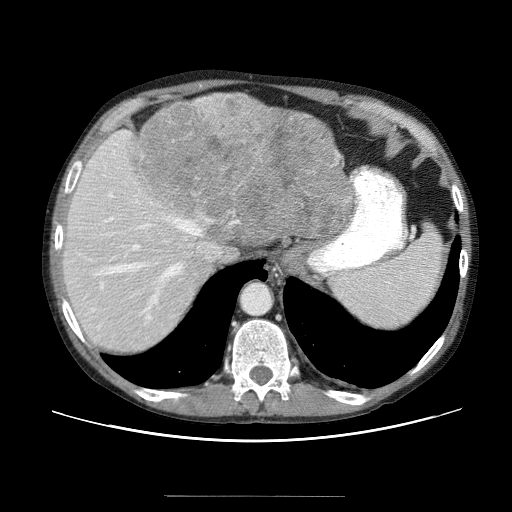
Contrast-enhanced abdominal CT (liver protocol), one axial slice; slice 46 of 69 in the series (ordered by position); reconstruction kernel STANDARD; soft-tissue window (W 400 / L 40 HU); 512 × 512 image matrix, field of view 380 × 380 mm. From the clinical record (not read from this slice): diagnosis: hepatocellular carcinoma (patient treated with transarterial chemoembolisation; whether this scan precedes or follows treatment is not stated here); TNM stage (as recorded): Stage-IVB; Child-Pugh class: B; tumour nodularity: multinodular.
Structures marked on this image (semi-automatically segmented with operator editing):
- liver parenchyma outside the tumour (the mass and vessels are separate outlines, so this box may not span the whole liver): box from (x=60, y=94) to (x=337, y=356) px
- mass: (x=137, y=93)–(x=356, y=262)
- liver vessels: (x=78, y=195)–(x=191, y=324)